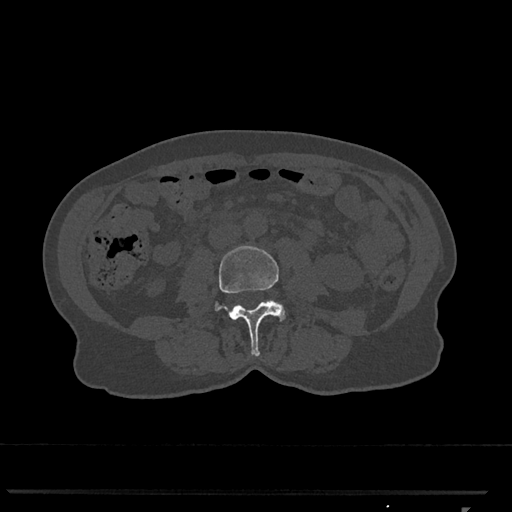
CT including the spine, one axial slice. Position 265 of 793 along the scan axis. Bone window (W 1800 / L 400 HU). 0.5 mm slice thickness. 512 × 512 image matrix, field of view 380 × 380 mm. Female patient, age 62 years. Case-level facts recorded for this patient, not image findings: primary cancer: renal.
Outlined on this slice (semi-automatic segmentation, software-assisted and operator-edited):
- L3 vertebra: box from (x=215, y=245) to (x=286, y=357) px